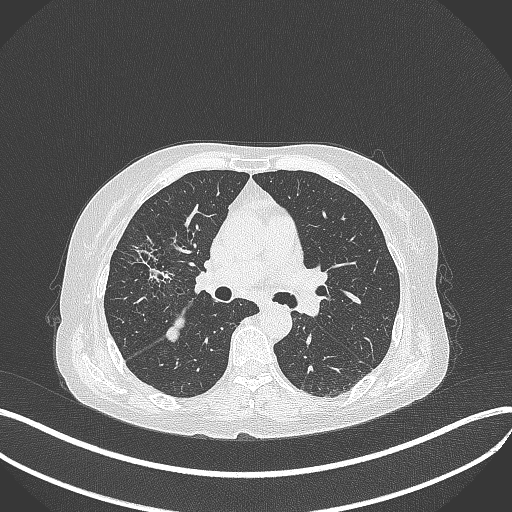
Chest CT, one axial slice; position 233 of 429 along the scan axis; reconstruction kernel B70f; lung window (W 1500 / L -600 HU); 512 × 512 image matrix, field of view 400 × 400 mm. Female patient, age 69 years. From the clinical record (not read from this slice): clinical TNM (as recorded): T1b N3 M0.
Outlined on this slice (rectangle marked by the reading radiologist):
- lung tumour (recorded histology: small cell carcinoma): bounding box <121,238,178,286> (left, top, right, bottom; pixels)